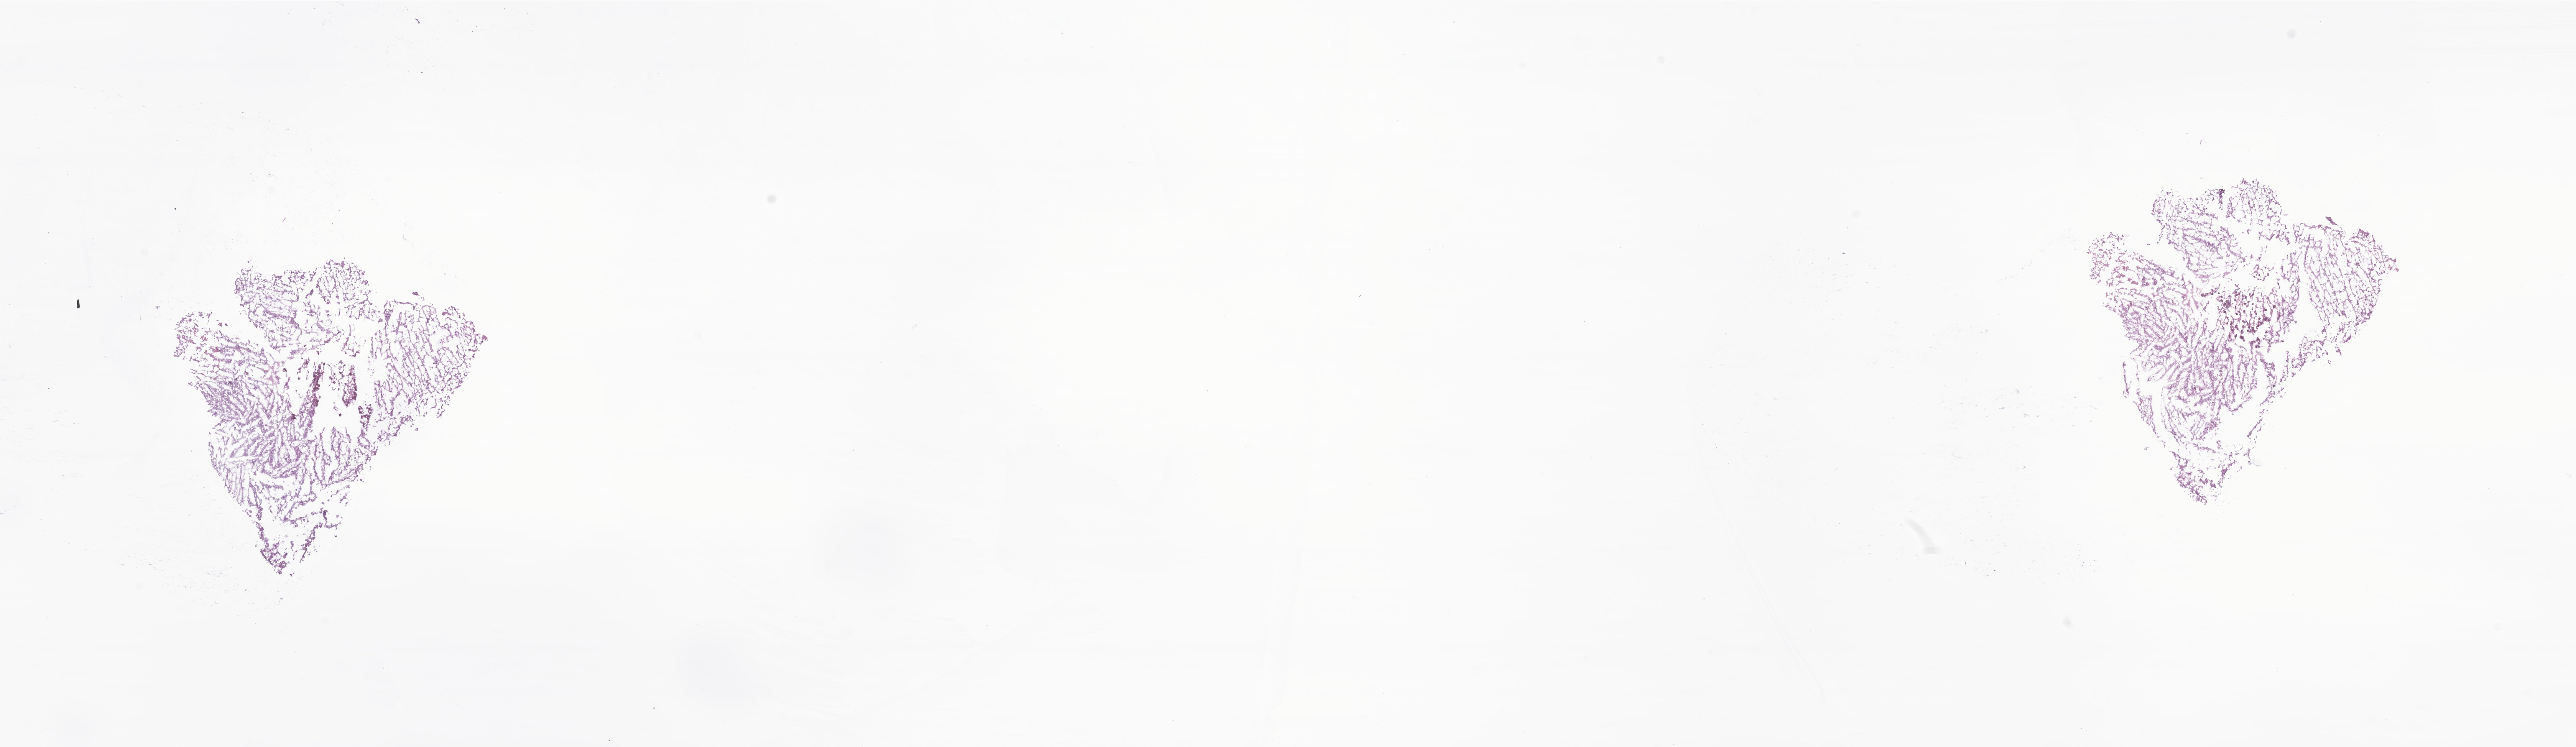
Digitized H&E-stained section of tumor tissue from the brain, whole scanned area (about 28.3 x 8.2 mm) shown as a low-resolution overview, cryosection (OCT / tissue freezing medium). Female patient, age 49 months (4 years 1 month).
Diagnosis: Neoplasm, uncertain whether benign or malignant.